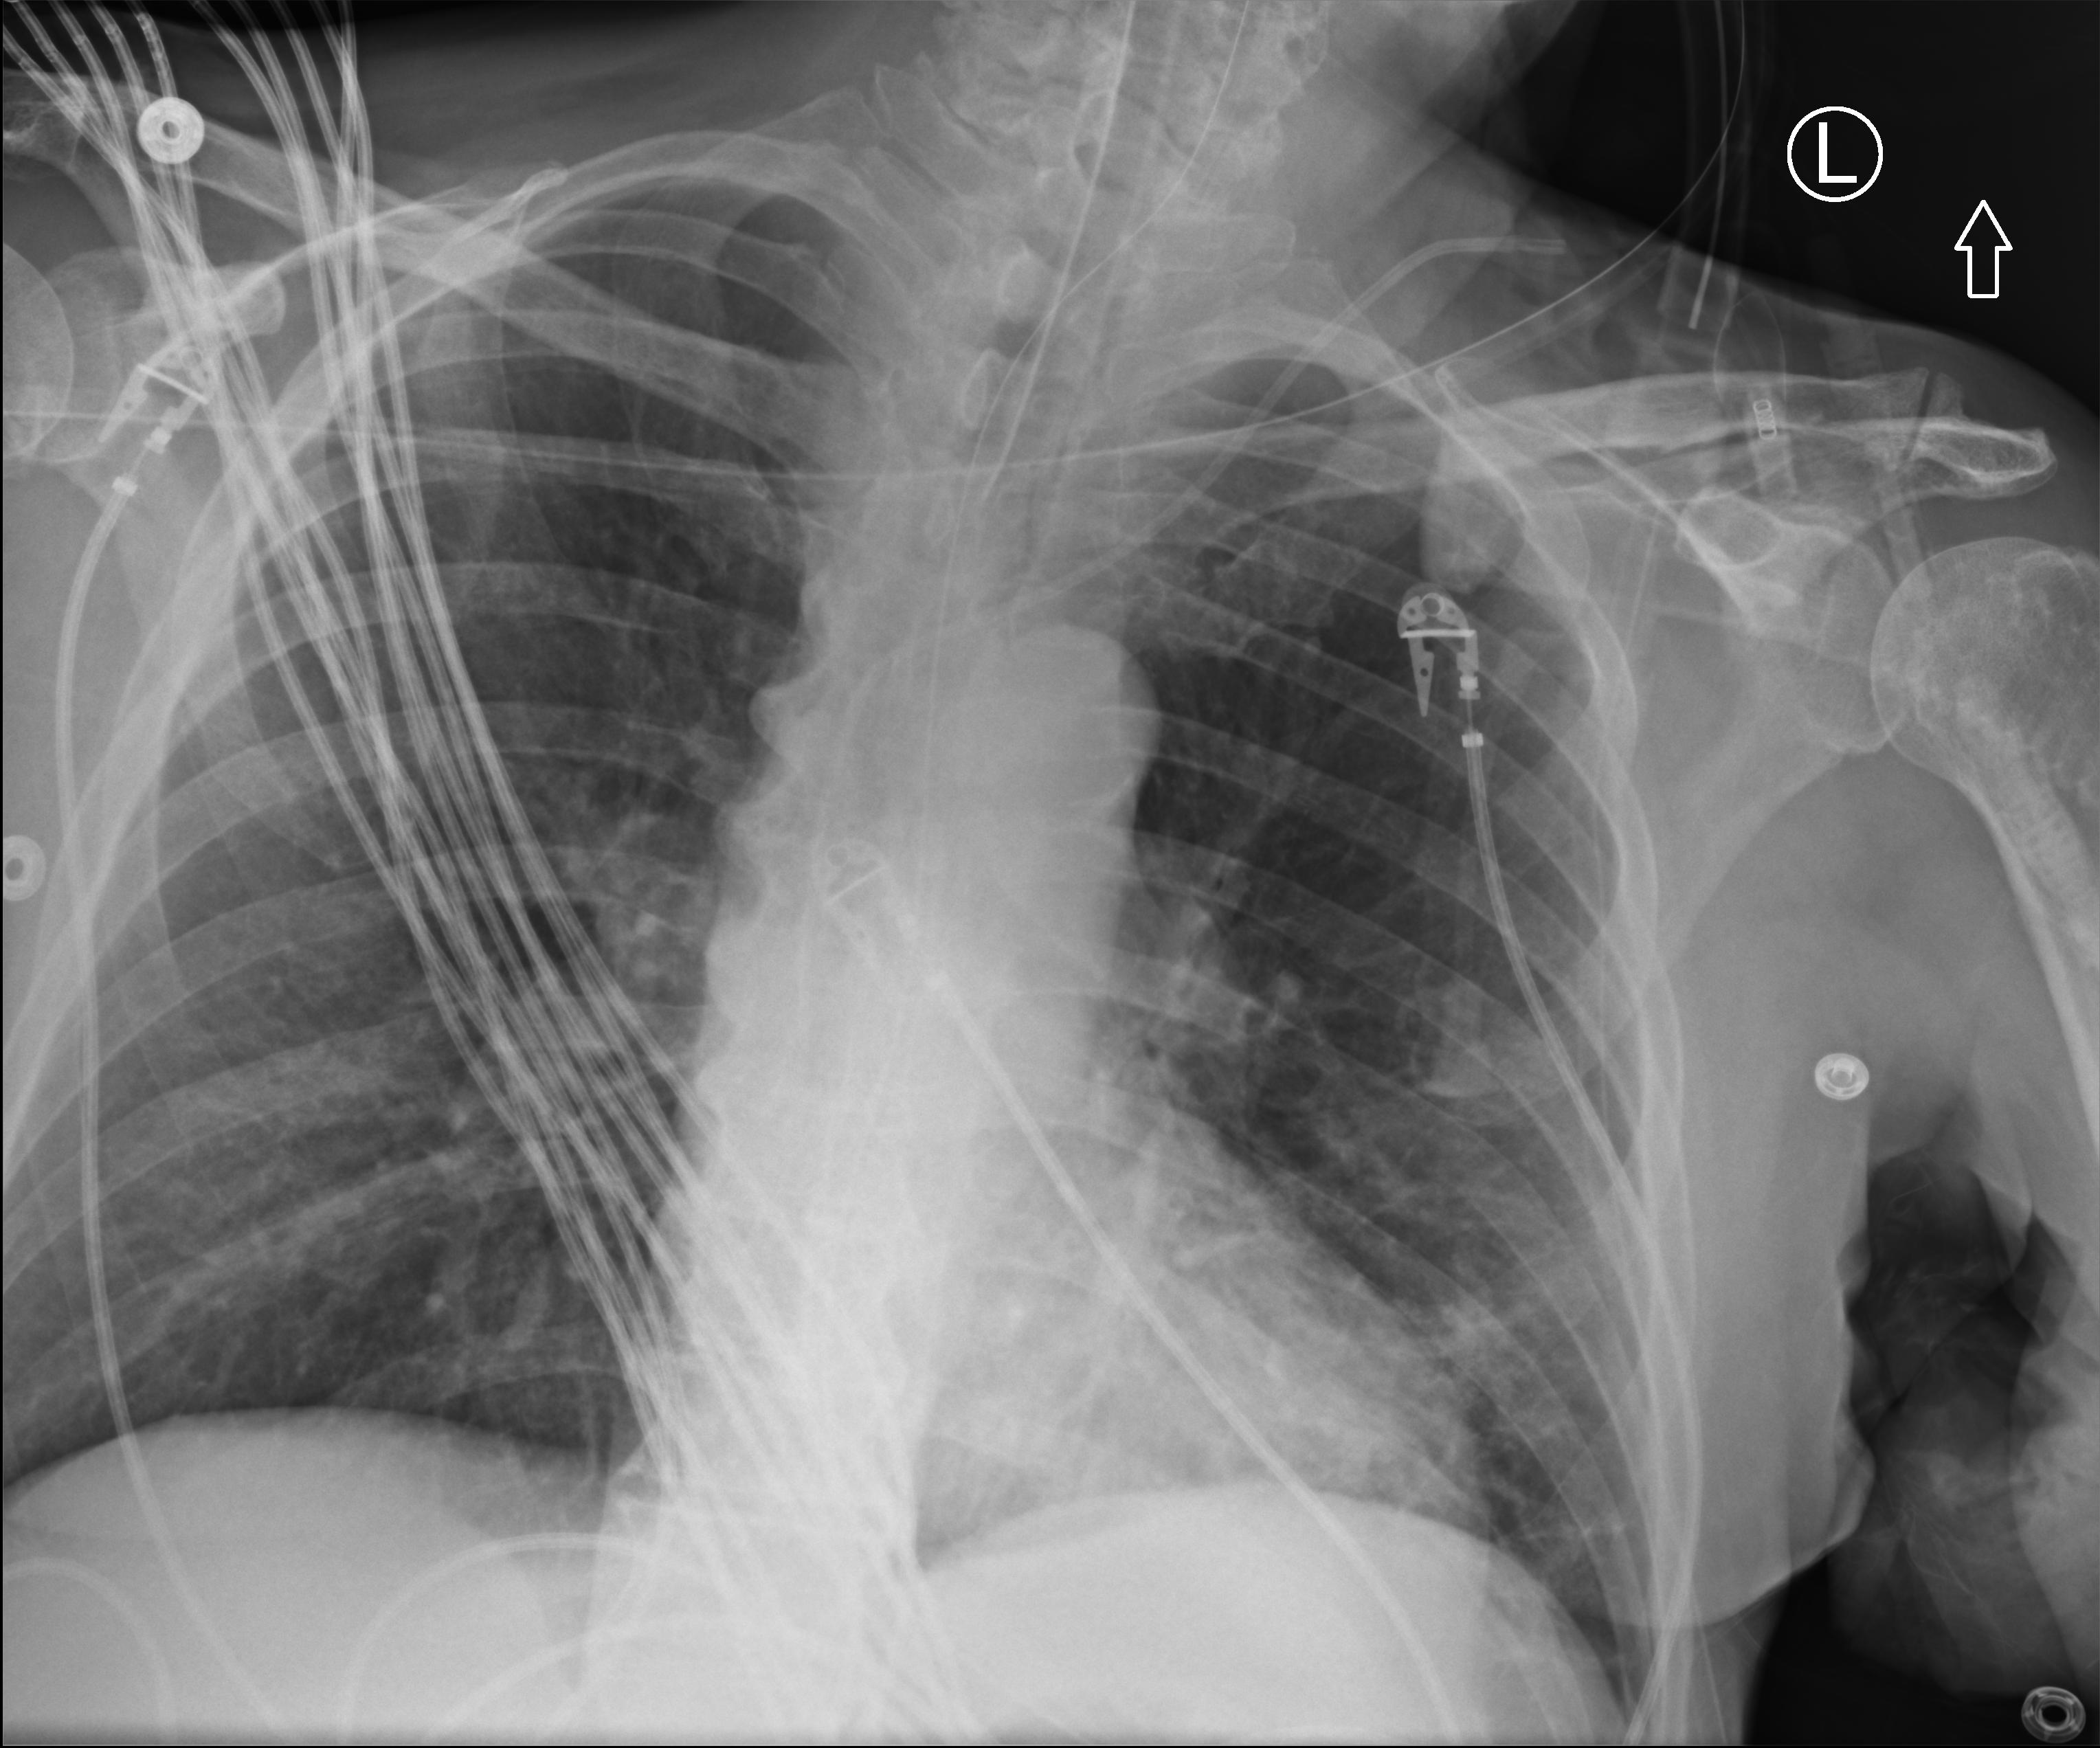
Portable chest radiograph; anteroposterior (AP) projection. Patient hospitalised with COVID-19; male, aged 60–74 years.
Hospital-stay facts (about this admission, not read from this image; timing relative to this image not recorded): mechanically ventilated during this hospital stay: yes; other chronic lung disease (admission record): no.